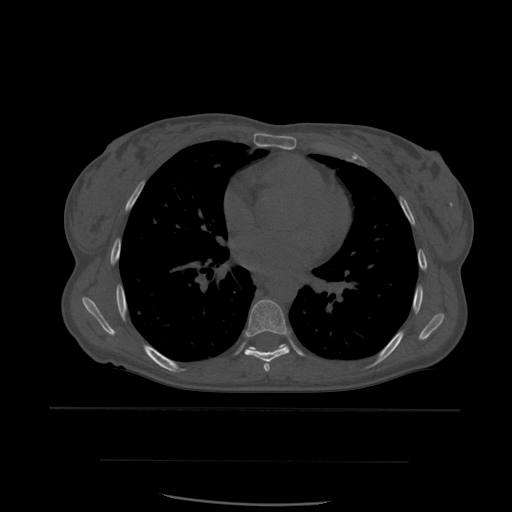
CT including the spine, one axial slice; position 371 of 574 along the scan axis; bone window (W 1800 / L 400 HU); 1.25 mm slice thickness; 512 × 512 image matrix, field of view 392 × 392 mm. Patient age 48 years. From the clinical record (not read from this slice): primary cancer: lung.
Structures marked on this image (semi-automatically segmented with operator editing):
- T6 vertebra: bounding box <264,364,270,372> (left, top, right, bottom; pixels)
- T7 vertebra: <244,300,290,371>
- T8 vertebra: <247,344,287,352>